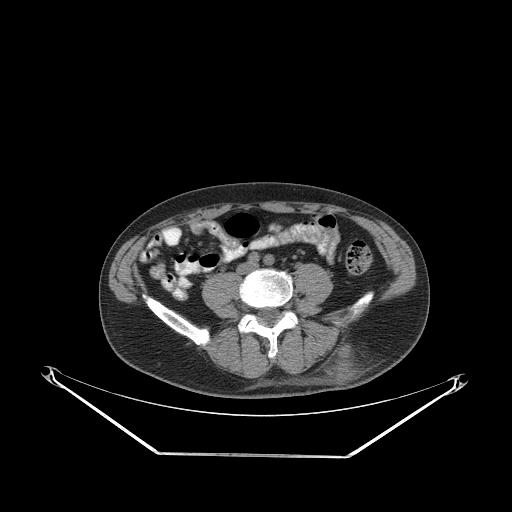
CT of an extremity soft-tissue mass (from a PET/CT study), one axial slice. Position 93 of 267 along the scan axis. Reconstruction kernel STANDARD. 140 kVp. Soft-tissue window (W 400 / L 40 HU). 512 × 512 image matrix, field of view 500 × 500 mm. Male patient. Case-level facts recorded for this patient, not image findings: histological type: leiomyosarcoma; grade: intermediate; site of the primary tumour: left pelvis.
Outlined on this slice (expert contour drawn on MRI and transferred to this co-registered scan by the dataset authors):
- gross tumour volume (mass): bounding box [x1, y1, x2, y2] px = [327, 342, 364, 382]